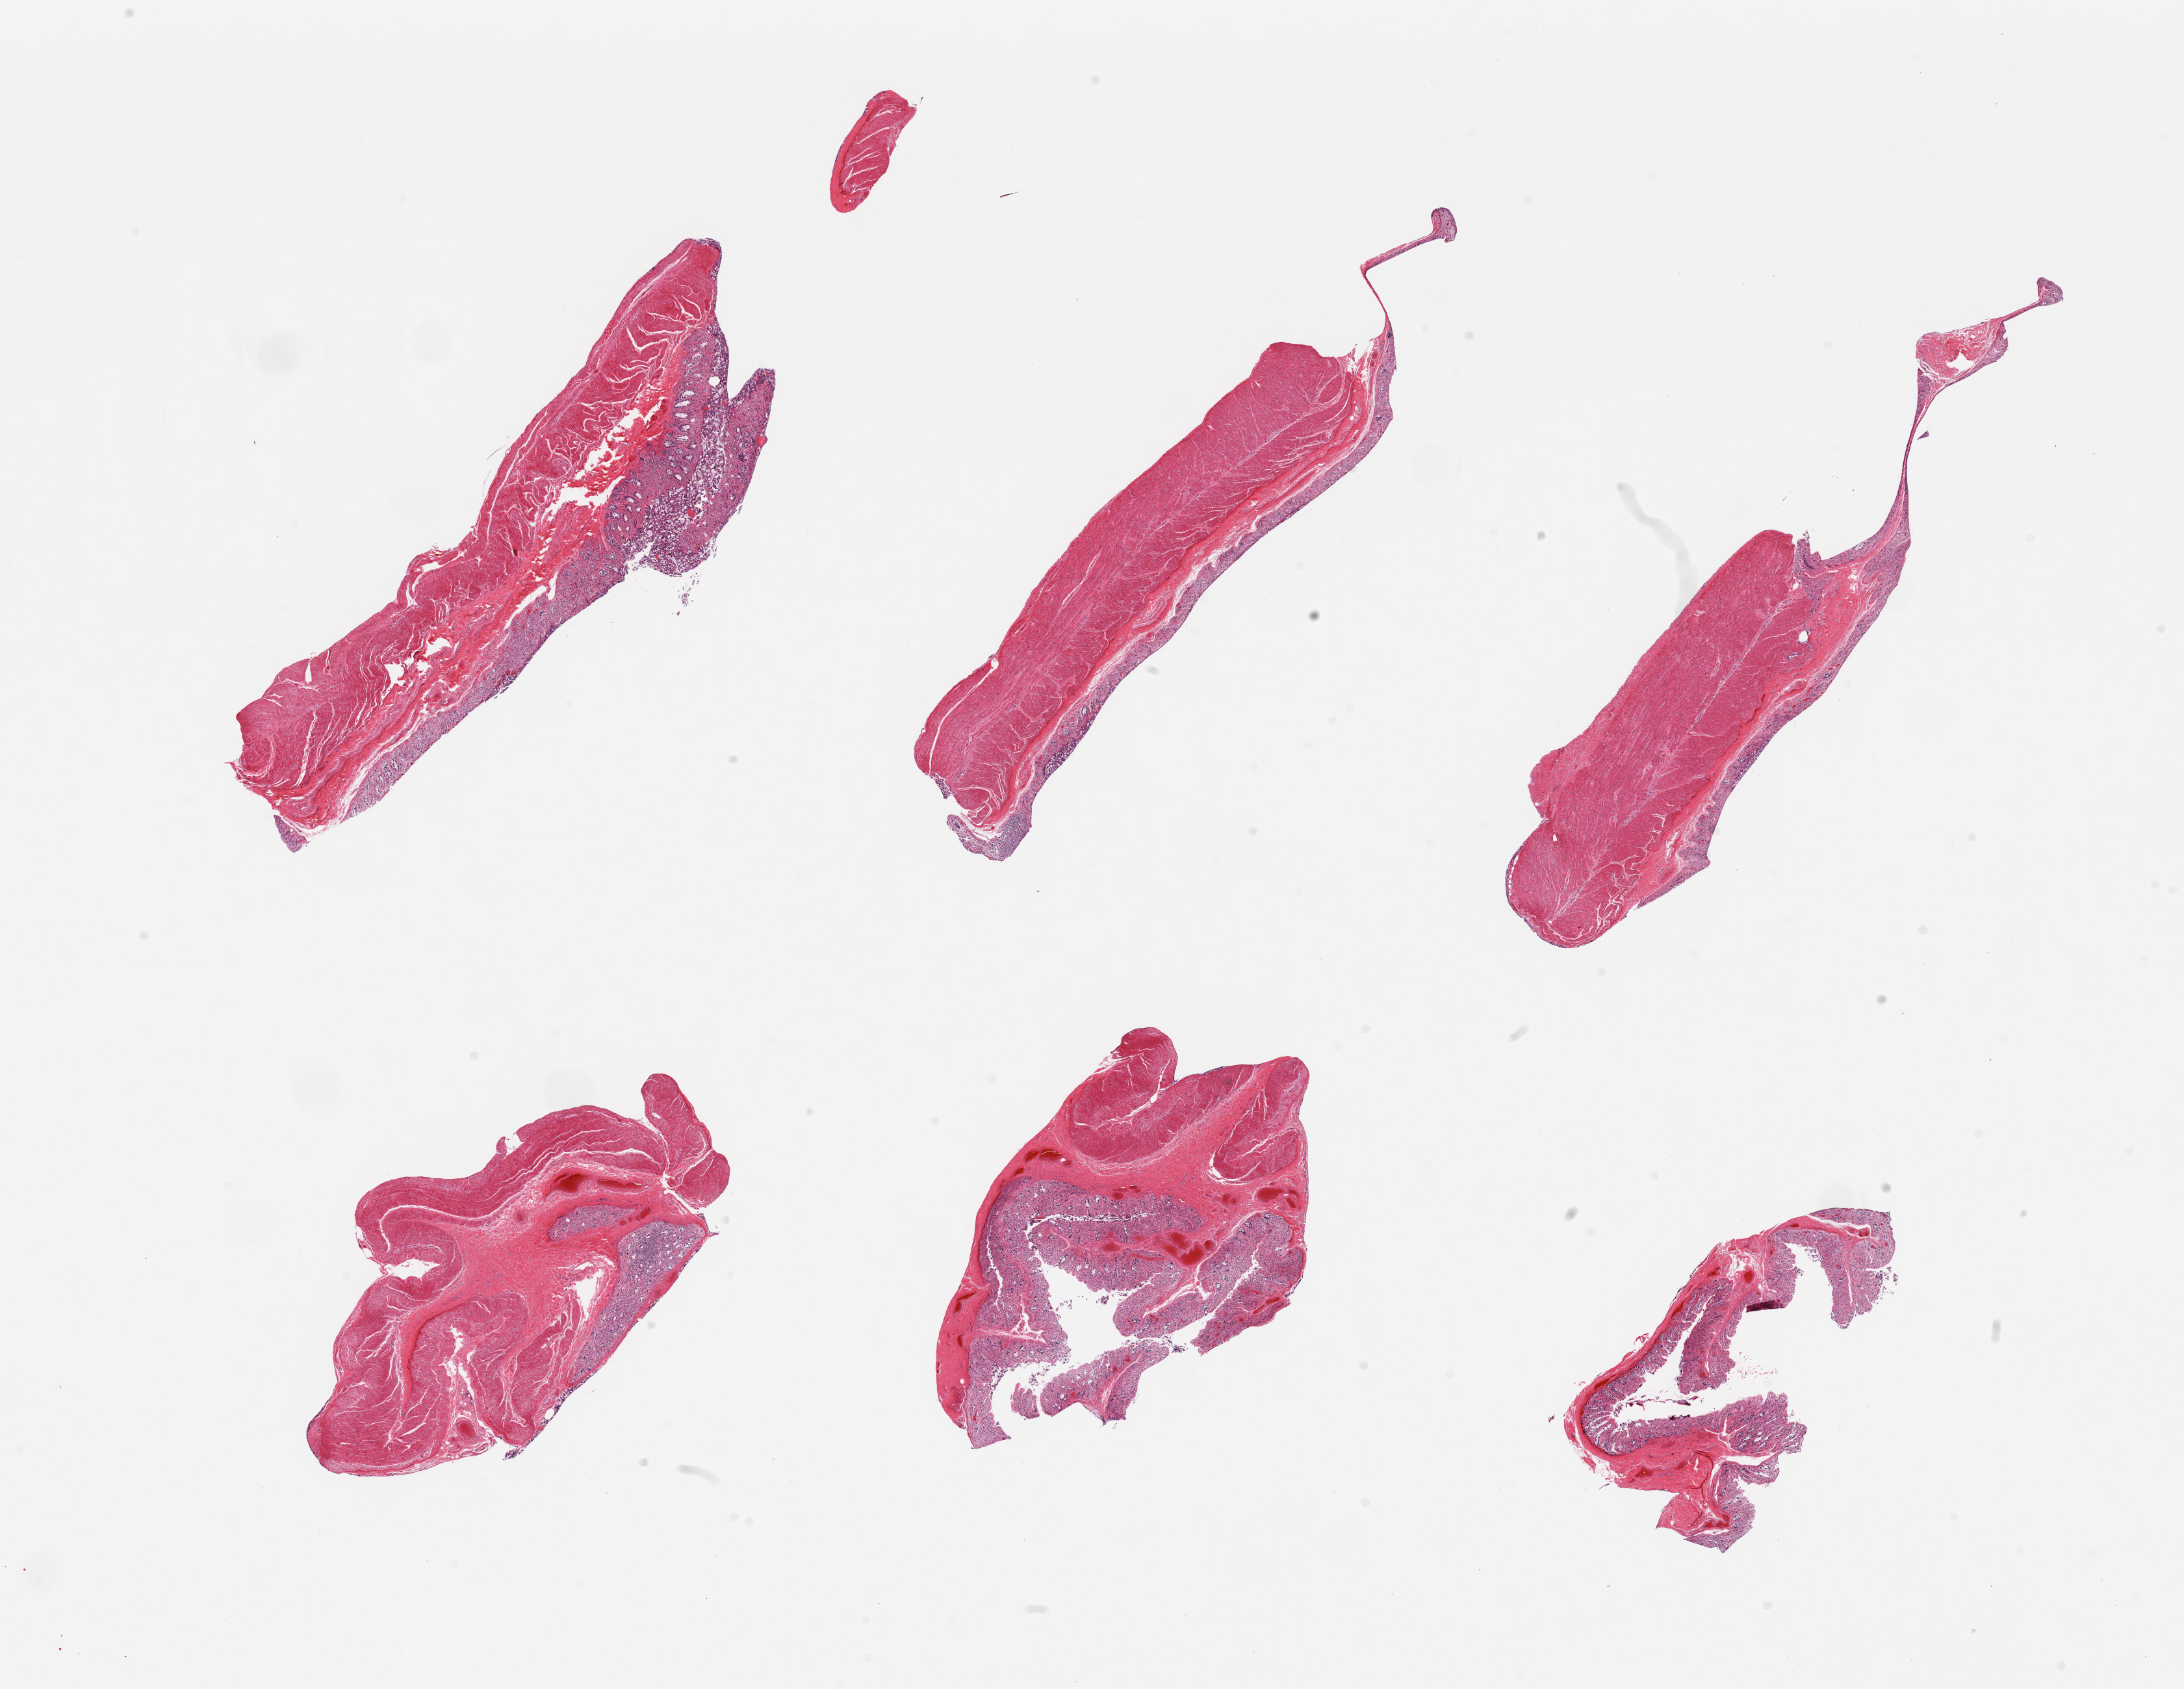
Haematoxylin and eosin whole-slide image, brightfield — shown as a low-resolution overview of the whole scanned area (about 26.6 x 20.6 mm); PAXgene-fixed, paraffin-embedded tissue; target tissue: transverse colon; donor tissue sample. Donor: male.
* pathologist's review note for this sample: 6 pieces, severely autolyzed mucosa (3) and muscularis (2)